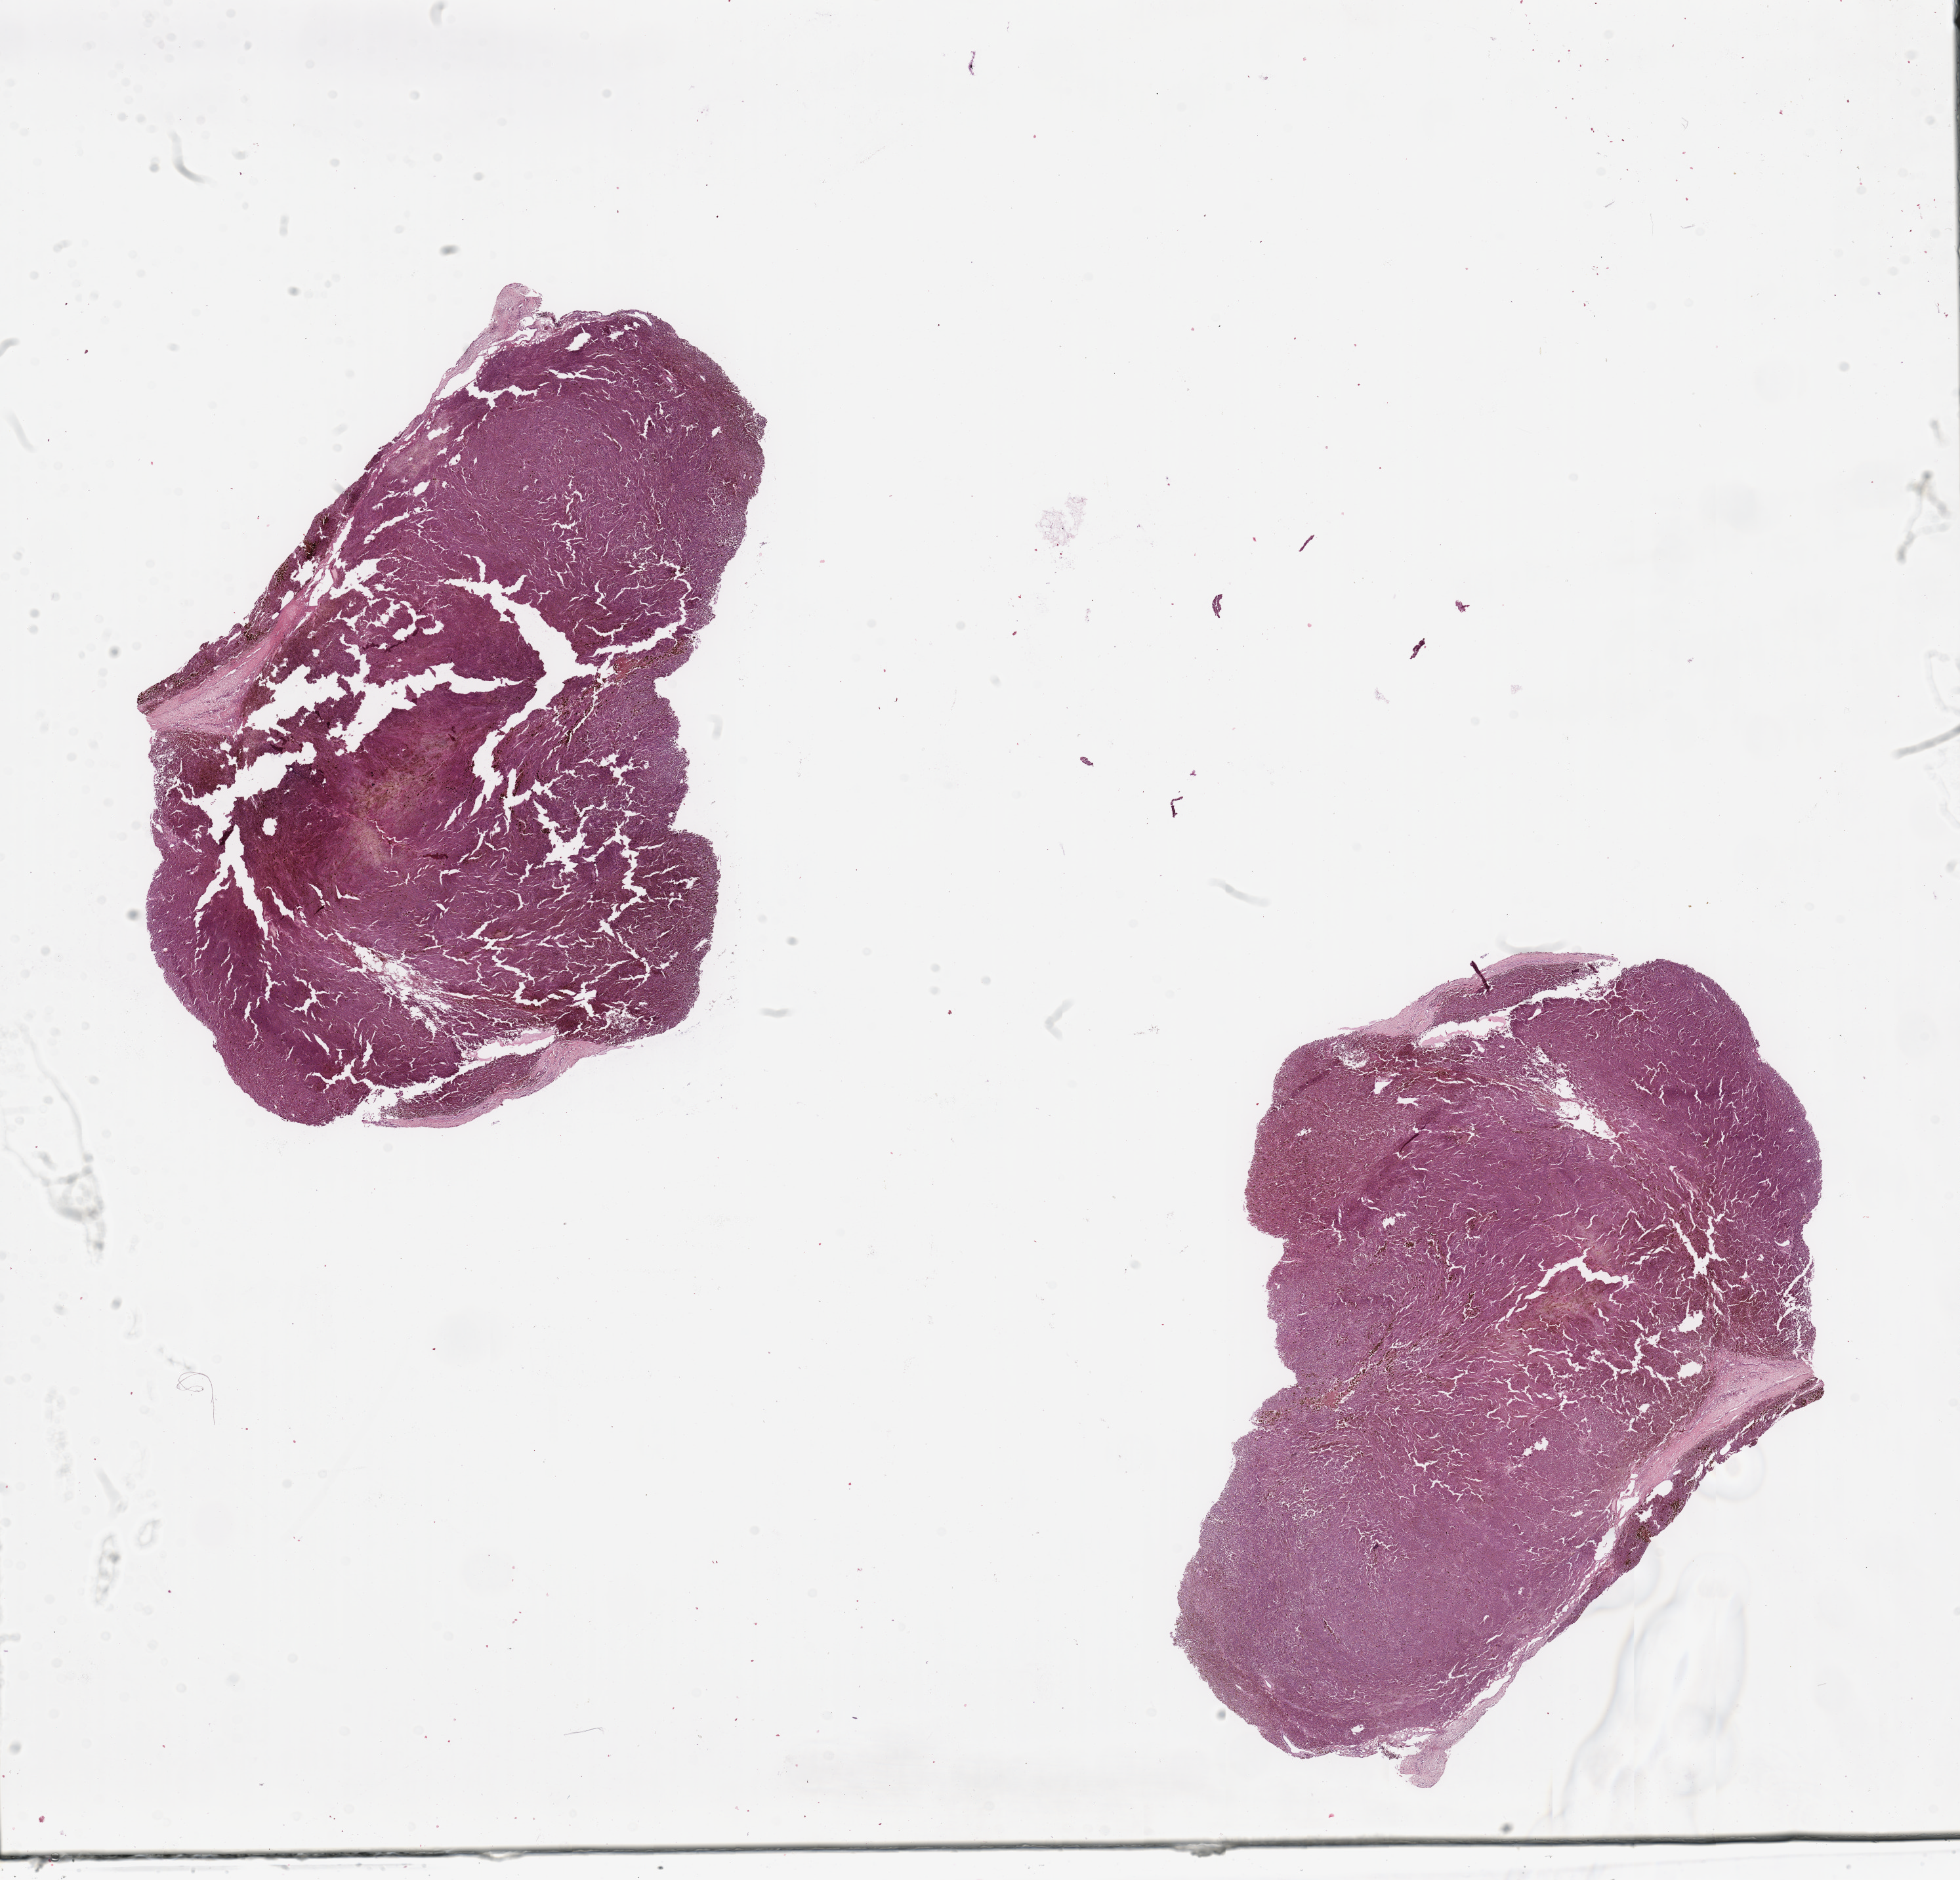
Digitized Hematoxylin and eosin (H&E) stained tissue section (whole slide), shown as a low-resolution overview of the whole scanned area (about 23.6 x 22.7 mm, slide scanned at 20x). Melanoma tumour tissue; sampled site not recorded. Female, 54 y/o.
Histologic diagnosis: Malignant melanoma, NOS.